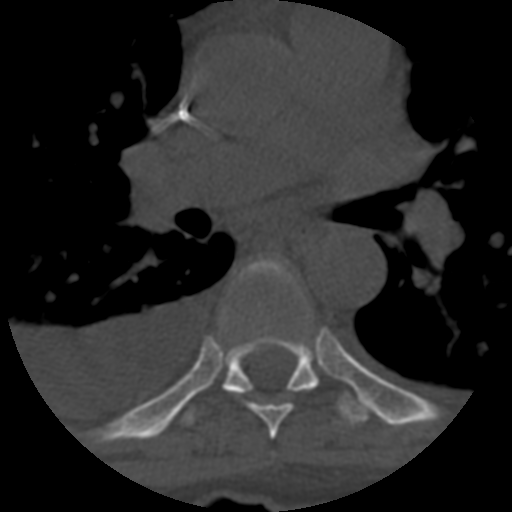
CT including the spine, one axial slice; slice 426 of 708 in the series (ordered by position); reconstruction kernel STANDARD; 120 kVp; one of 3 acquisitions stored at this slice position; bone window (W 1800 / L 400 HU); 1.25 mm slice thickness; 512 × 512 image matrix. Patient age 55 years. Case-level facts recorded for this patient, not image findings: primary cancer: colon; vertebrae with lytic lesions (as recorded): T12, L1, L5.
Outlined on this slice (semi-automatic segmentation, software-assisted and operator-edited):
- T6 vertebra: box from (x=249, y=328) to (x=292, y=439) px
- T7 vertebra: (x=182, y=258)–(x=369, y=426)